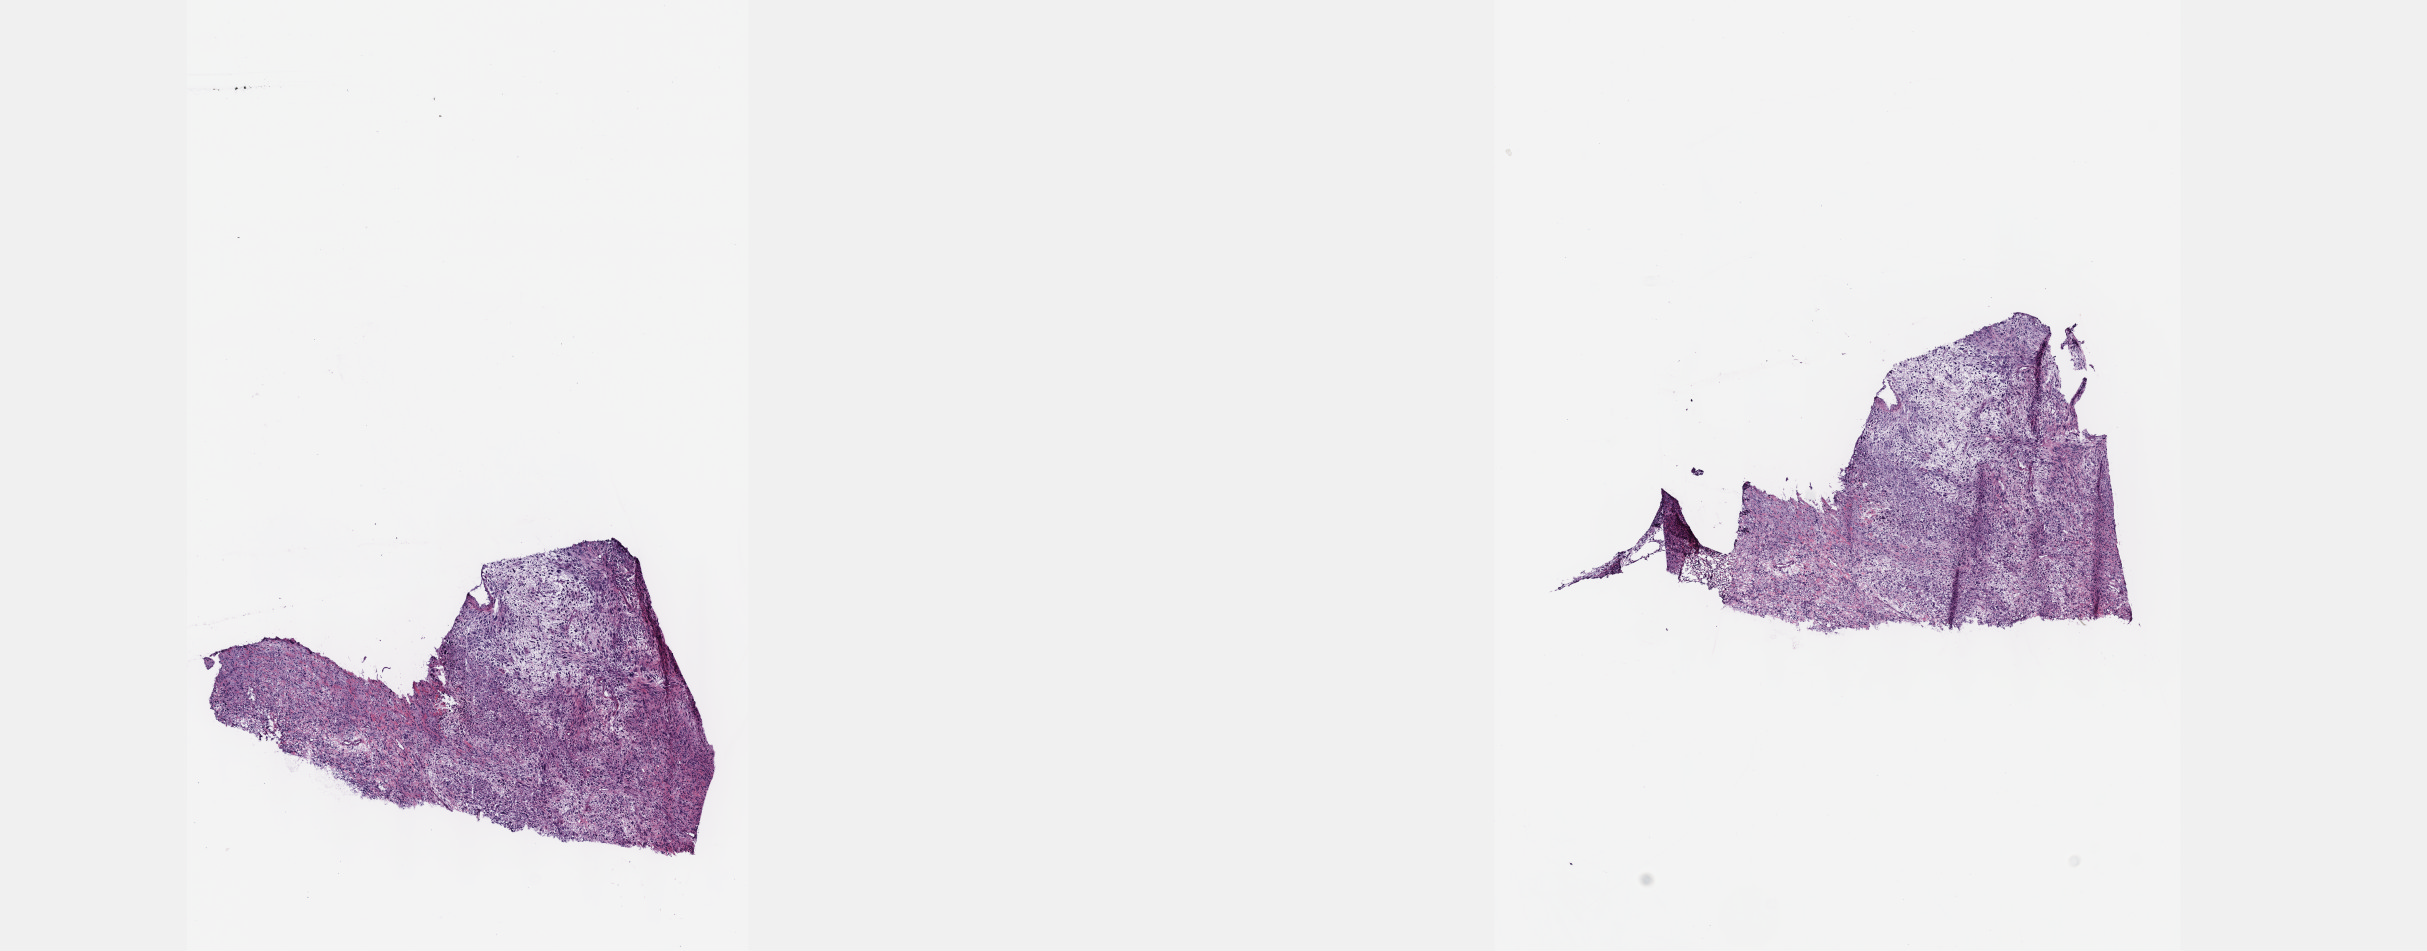
H&E-stained whole-slide image — whole scanned area (about 19.6 x 7.7 mm) shown as a low-resolution overview. Frozen section from the top of the tissue portion. Connective, subcutaneous and other soft tissues, primary tumour sample. Patient: male, age at initial diagnosis 55 years.
Pathologic diagnosis: Fibromyxosarcoma (connective, subcutaneous and other soft tissues of lower limb and hip).